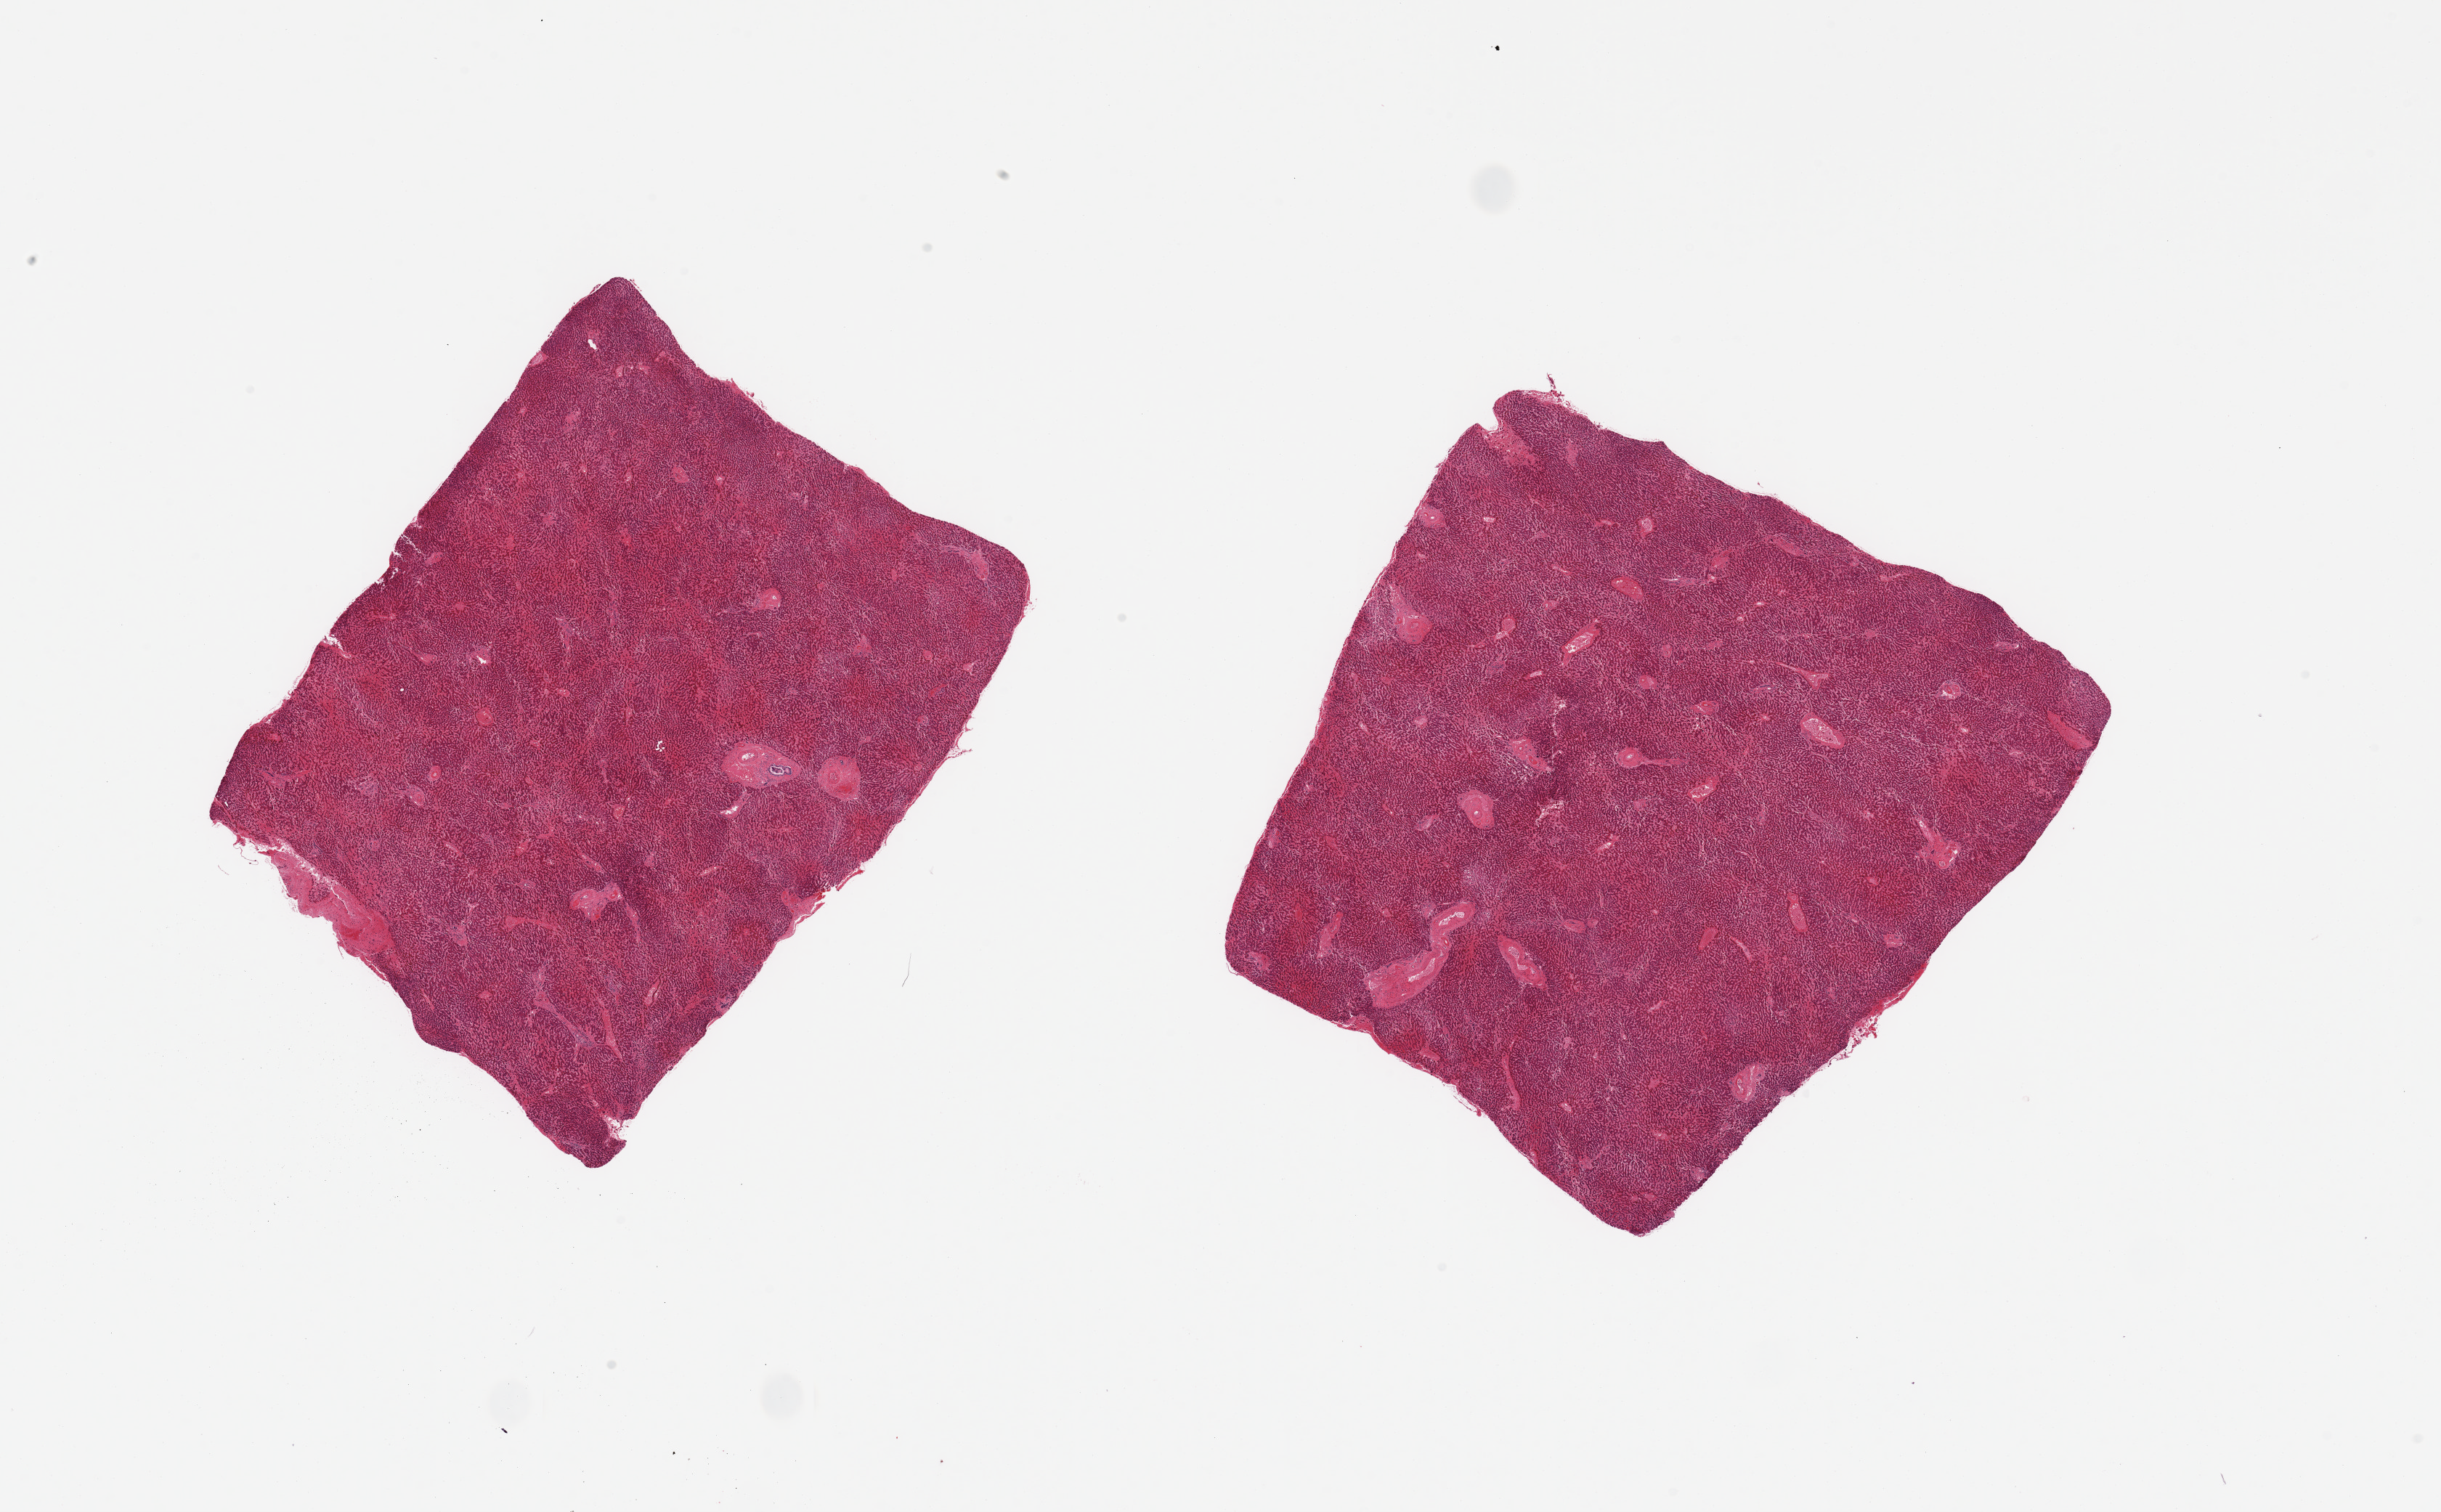
H&E whole-slide image — shown as a low-resolution overview of the whole scanned area (about 26.6 x 16.5 mm); PAXgene-fixed, paraffin-embedded tissue; sampled site (target tissue): liver; donor tissue sample. Female donor.
Pathologist's review note for this sample: 2 pieces, moderate diffuse passive congestion.